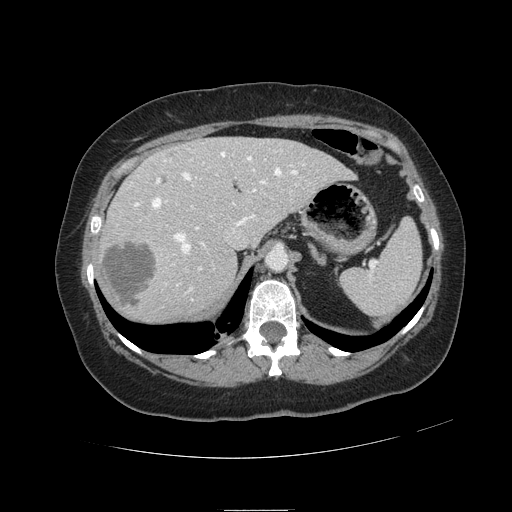
Contrast-enhanced abdominal CT, one axial slice; slice 80 of 121 in the series (ordered by position); 120 kVp; intravenous contrast given; soft-tissue window (W 400 / L 40 HU); 2.5 mm slice thickness; 512 × 512 image matrix, field of view 400 × 400 mm. Female patient, age 52 years. From the clinical record (not read from this slice): diagnosis: colorectal cancer liver metastases, imaged before liver resection; multiple liver metastases: yes; largest metastasis: 6.3 cm; disease in both lobes: no.
Annotated regions visible in this slice (expert manual segmentation):
- hepatic veins: bounding box <135,150,305,300> (left, top, right, bottom; pixels)
- liver: <100,137,350,321>
- planned liver remnant (the part of the liver to remain after resection): <168,137,350,241>
- portal vein (with intrahepatic branches): <156,159,267,292>
- liver metastasis: <102,240,157,307>